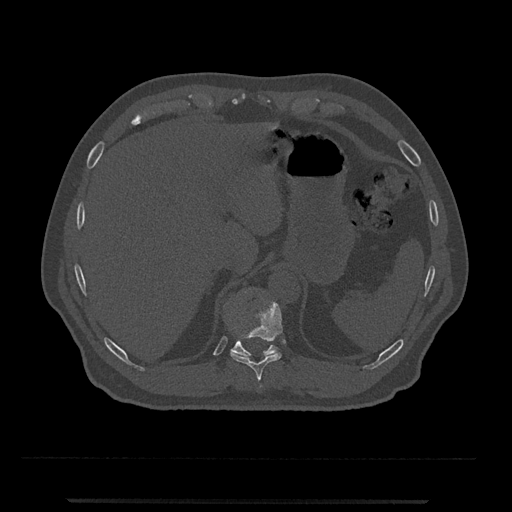
CT including the spine, one axial slice. Reconstruction kernel Br40s/3. 120 kVp. Bone window (W 1800 / L 400 HU). 0.5 mm slice thickness. 512 × 512 image matrix, field of view 419 × 419 mm. Patient: male, 63 years. From the clinical record (not read from this slice): primary cancer: prostate.
Annotated regions visible in this slice (semi-automatic segmentation, software-assisted and operator-edited):
- T10 vertebra: bounding box [x1, y1, x2, y2] px = [231, 301, 283, 382]
- T11 vertebra: [228, 288, 278, 356]